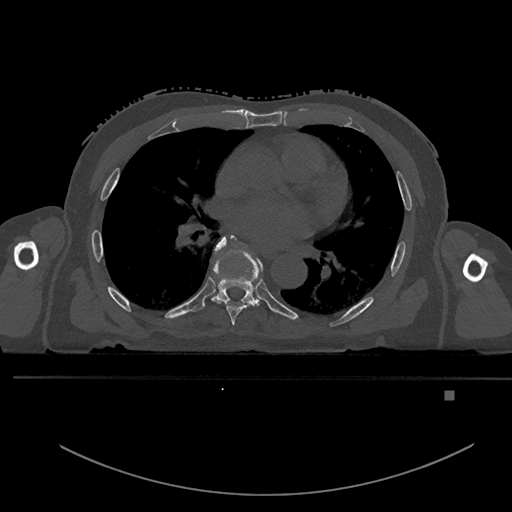
CT including the spine, one axial slice. Bone window (W 1800 / L 400 HU). 0.5 mm slice thickness. 512 × 512 image matrix, field of view 456 × 456 mm. Male patient, age 82 years. Case-level facts recorded for this patient, not image findings: primary cancer: prostate.
Structures marked on this image (semi-automatically segmented with operator editing):
- T6 vertebra: box from (x=211, y=236) to (x=259, y=325) px
- T7 vertebra: (x=213, y=240)–(x=261, y=306)